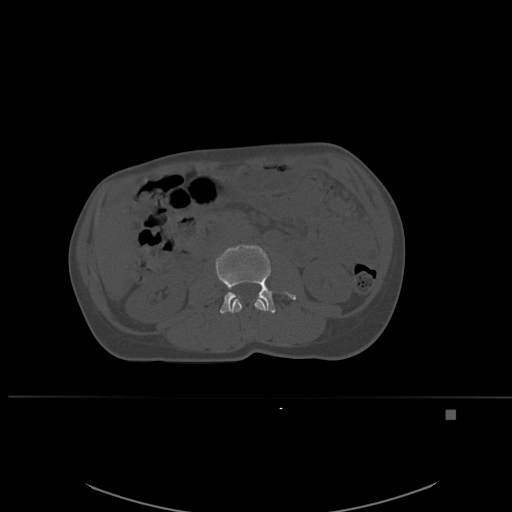
CT including the spine, one axial slice. Position 222 of 537 along the scan axis. Bone window (W 1800 / L 400 HU). 1.5 mm slice thickness. 512 × 512 image matrix. Patient: female, 45 years. From the clinical record (not read from this slice): primary cancer: lung.
Annotated regions visible in this slice (semi-automatically segmented with operator editing):
- L2 vertebra: bounding box (x1, y1, x2, y2) in pixels: (230, 296, 268, 313)
- L3 vertebra: (215, 245, 297, 314)